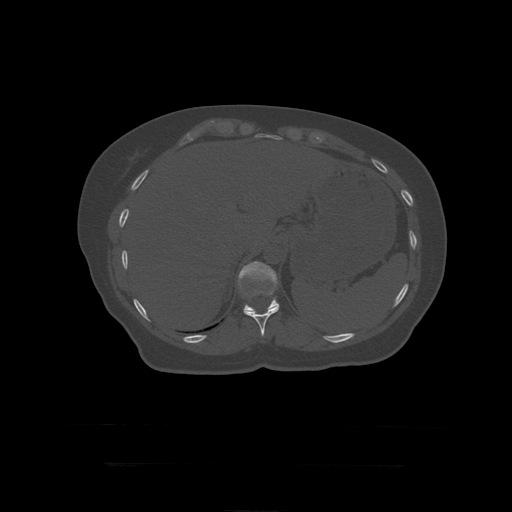
CT including the spine, one axial slice; slice 212 of 399 in the series (ordered by position); reconstruction kernel STANDARD; bone window (W 1800 / L 400 HU); 1.25 mm slice thickness; 512 × 512 image matrix, field of view 450 × 450 mm. Patient age 41 years. From the clinical record (not read from this slice): primary cancer: breast.
Structures marked on this image (semi-automatic segmentation, software-assisted and operator-edited):
- T11 vertebra: bounding box <244,305,280,337> (left, top, right, bottom; pixels)
- T12 vertebra: <238,262,279,312>